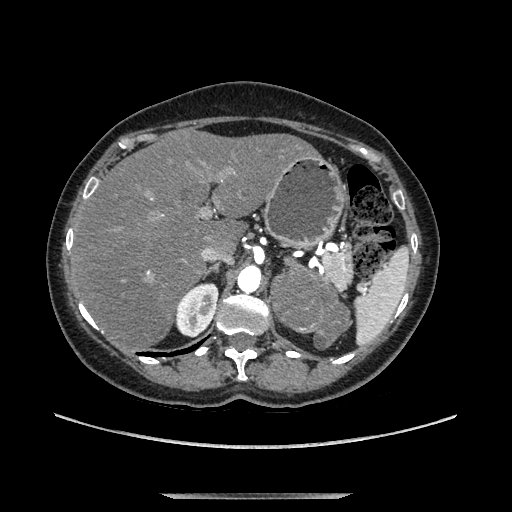
Contrast-enhanced abdominal CT, one axial slice; position 87 of 169 along the scan axis; soft-tissue window (W 400 / L 40 HU); 1.25 mm slice thickness; 512 × 512 image matrix. Female patient. From the clinical record (not read from this slice): diagnosis: adrenocortical carcinoma; tumour side: left adrenal; tumour size at pathology: 9 cm; Ki-67 index: 2 %; stage (as recorded): 3.
Structures marked on this image (semi-automatic segmentation, software-assisted and operator-edited):
- mass: bounding box <274,260,347,347> (left, top, right, bottom; pixels)